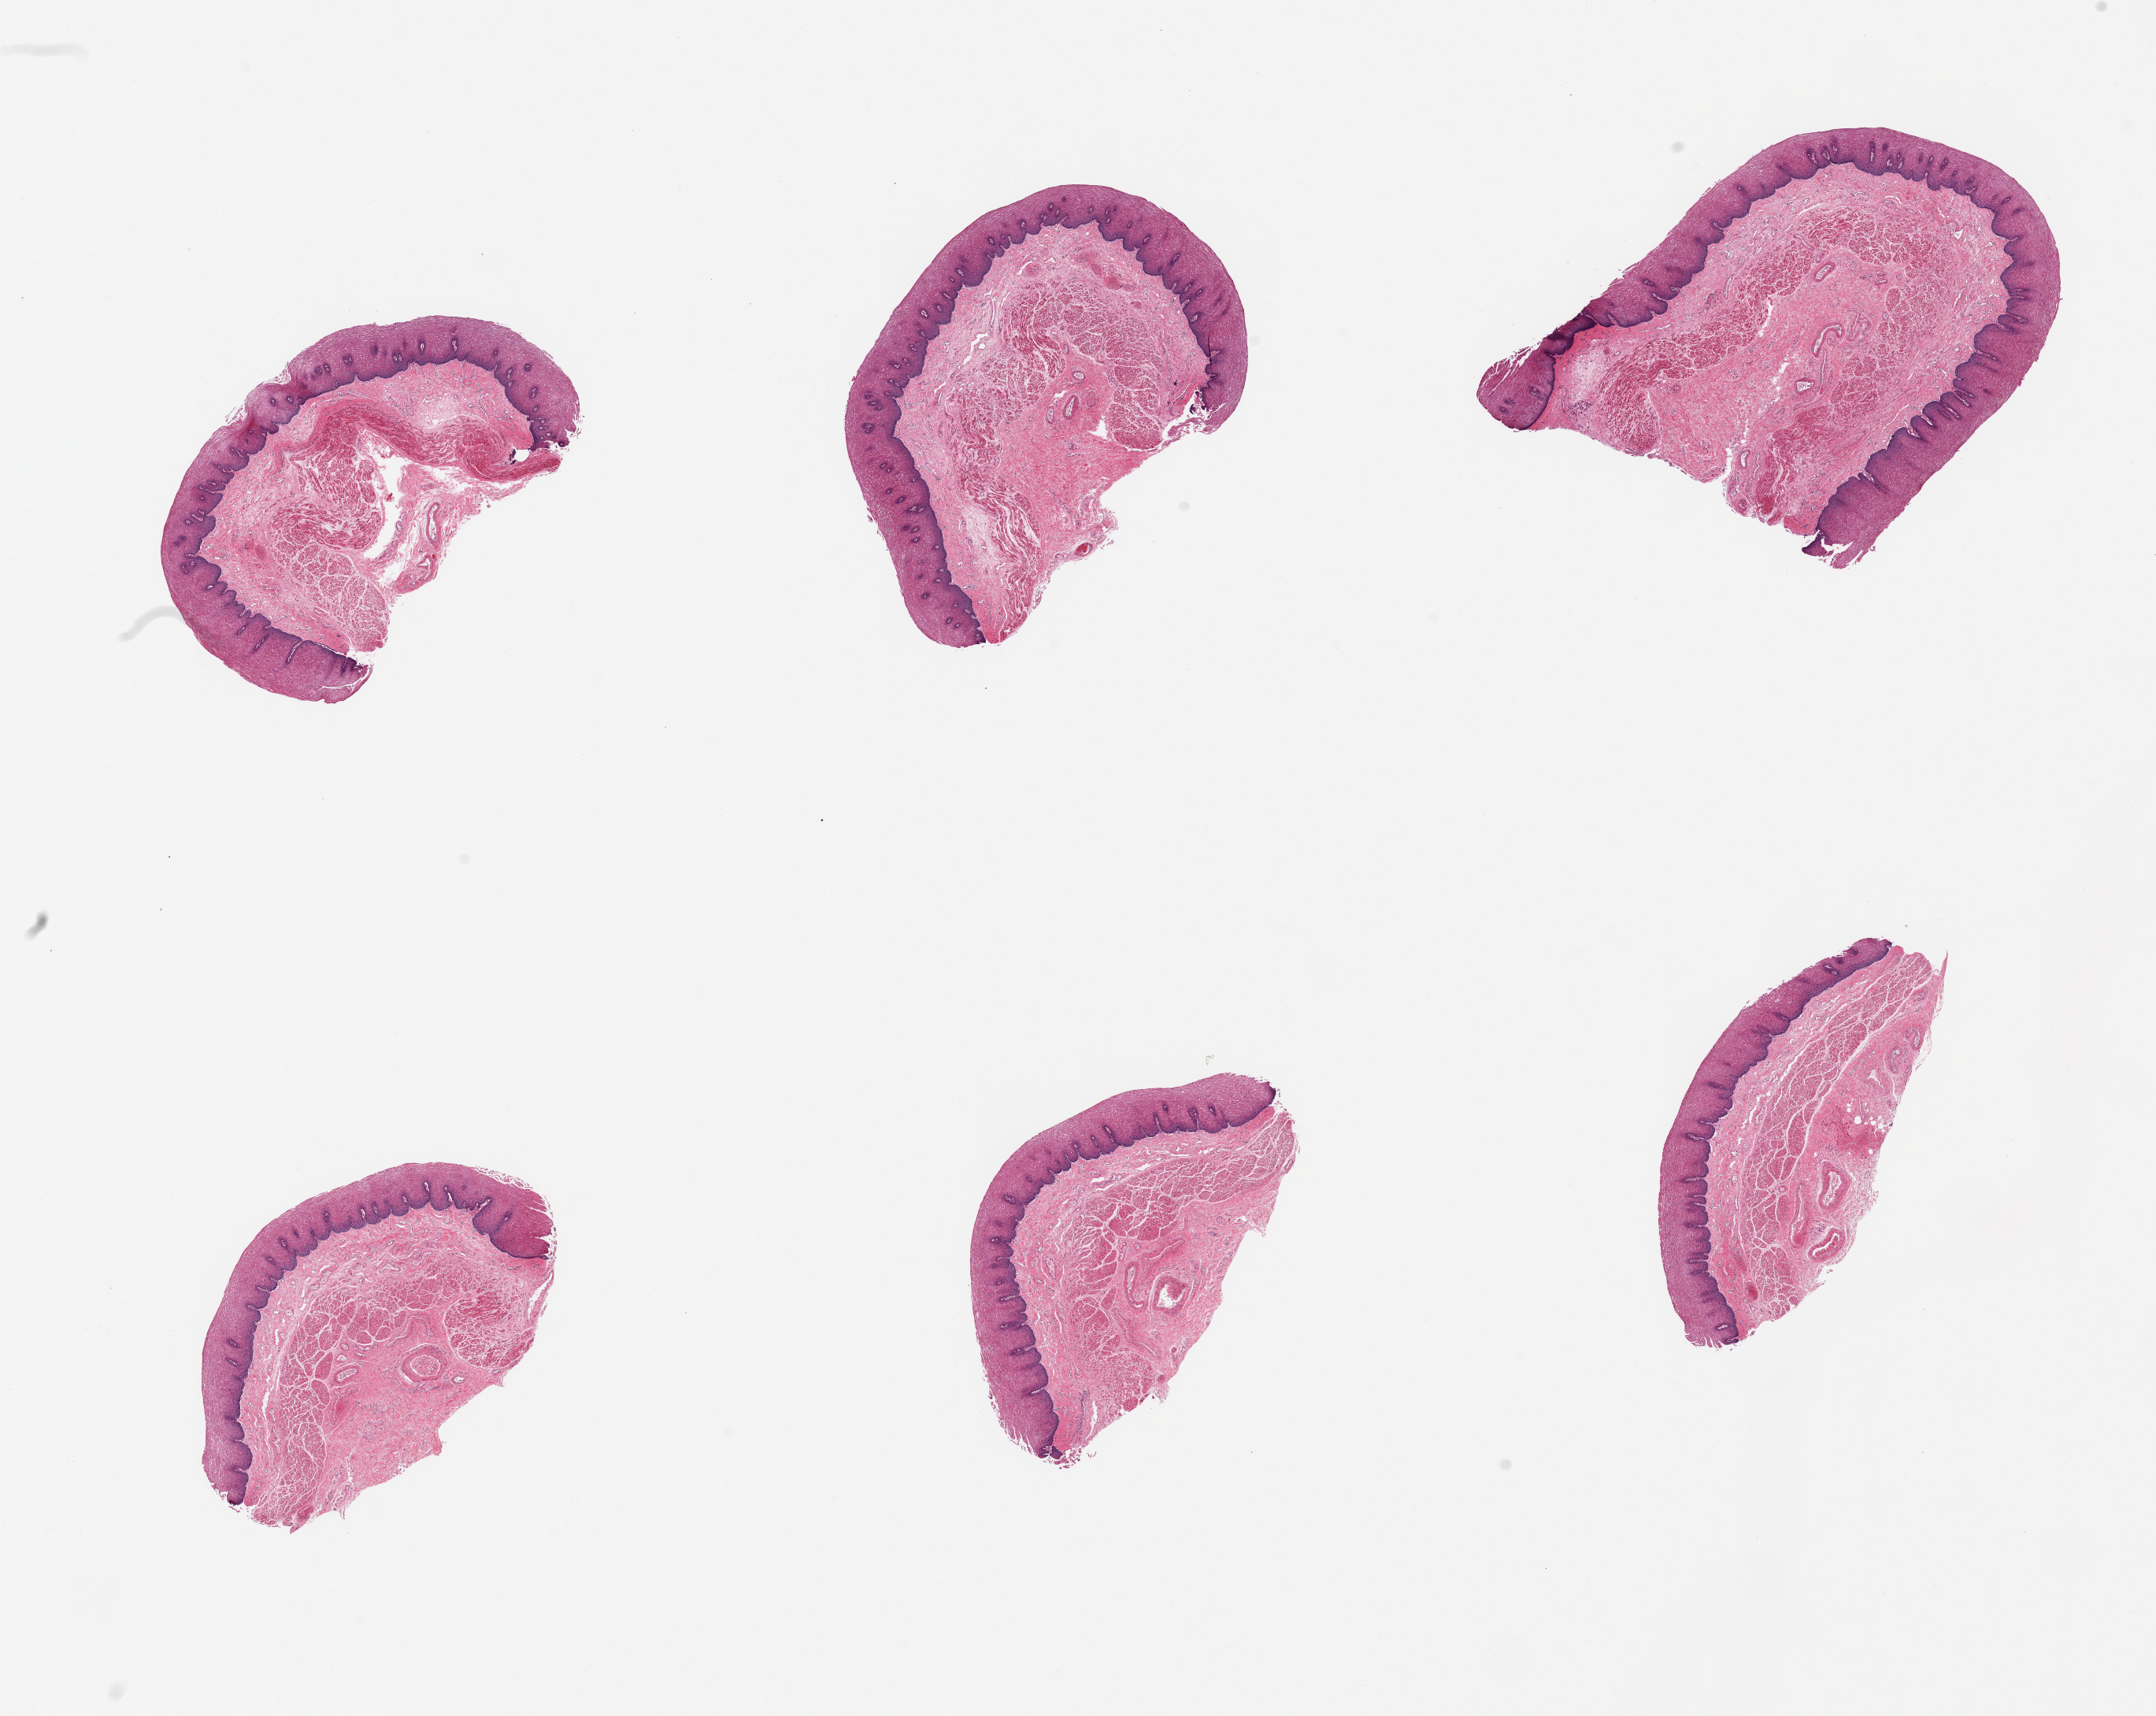
Hematoxylin and eosin (H&E) whole-slide image, brightfield — a low-resolution overview of the entire scanned area, about 21.7 x 17.2 mm; PAXgene-fixed, paraffin-embedded tissue; sampled site (target tissue): esophageal mucous membrane; tissue donor sample.
- review note (as recorded): 6 pieces, squamous mucosa is ~10-15% thickness